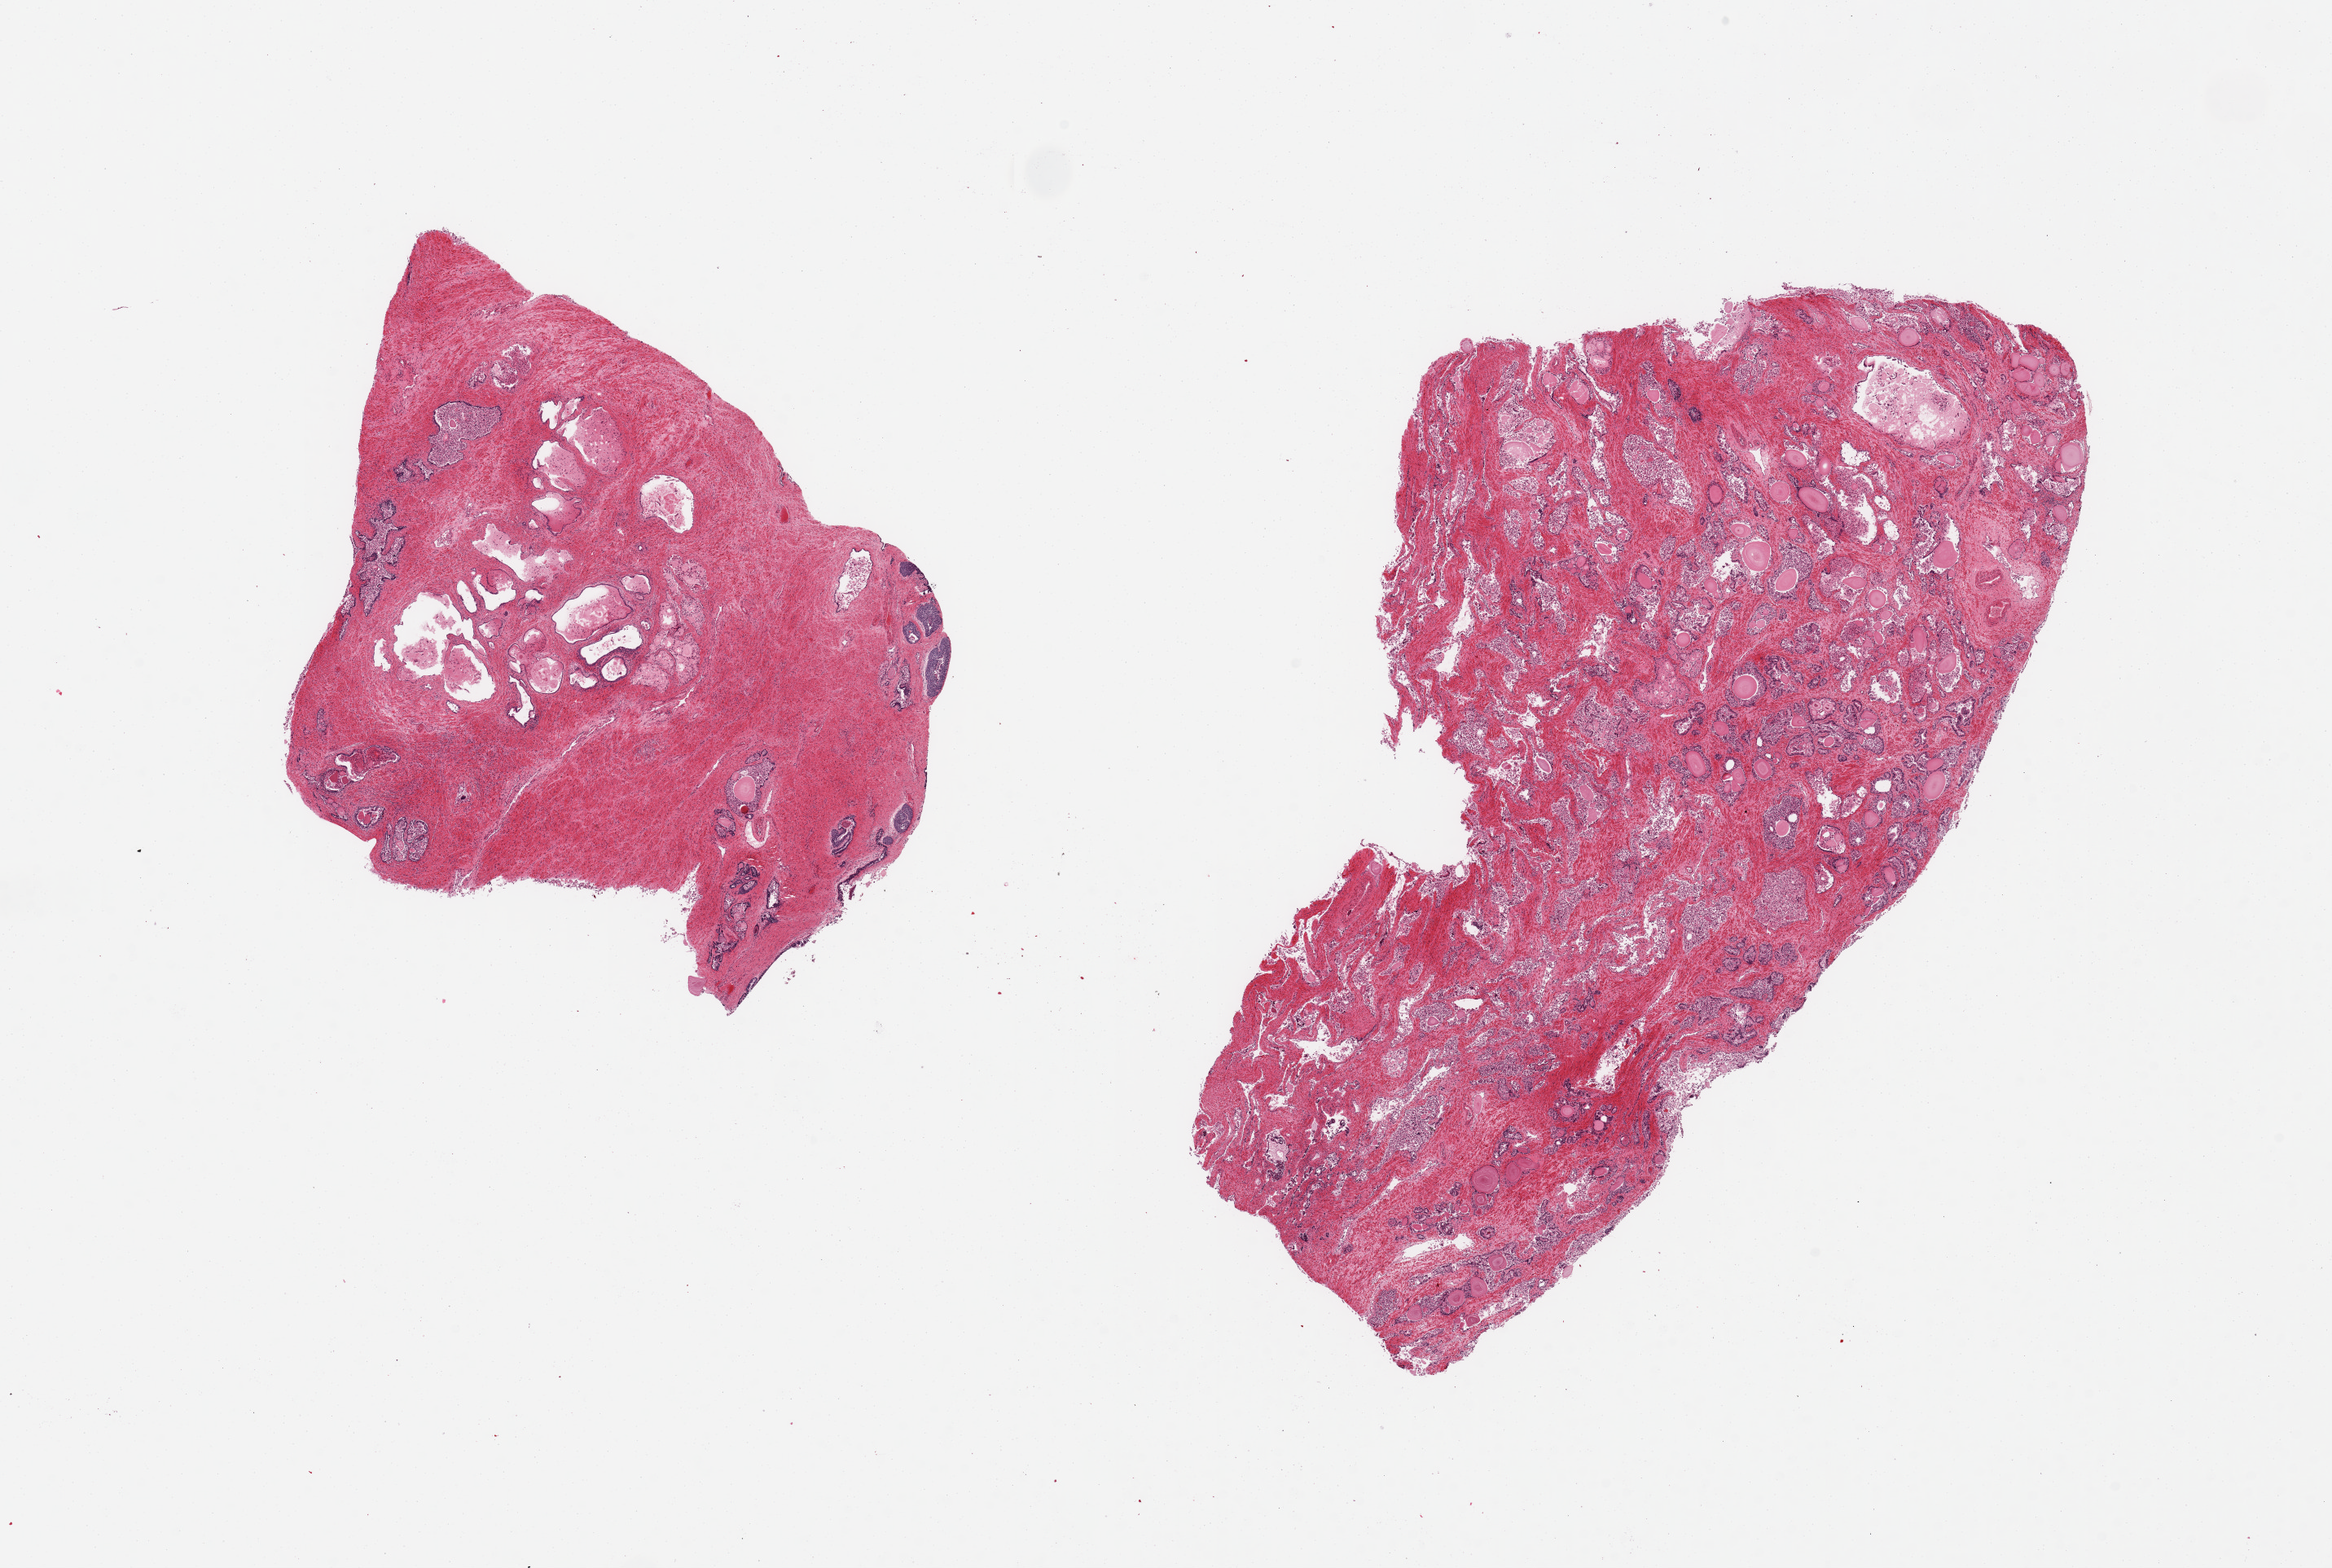
Digitized hematoxylin and eosin (H&E)-stained section, brightfield — low-resolution overview of the scanned area, about 22.6 x 15.2 mm (acquisition: 20x scan); PAXgene-fixed paraffin-embedded (PFPE) section; section of prostate (target tissue); tissue donor sample. Male donor.
• pathologist's review note for this sample: 2 pieces; glands autolyzed; stroma better preserved; 1 piece partially contains prostatic urethra and associated structures